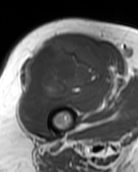
MRI of an extremity soft-tissue mass, one axial slice; position 69 of 99 along the scan axis; MR volume resampled by the dataset authors to the PET/CT grid (not the native acquisition matrix); 3.27 mm slice thickness; 138 × 172 image matrix, field of view 135 × 168 mm. Female patient. From the clinical record (not read from this slice): histological type: pleiomorphic undifferentiated sarcoma; grade: high; site of the primary tumour: right quadricep.
Annotated regions visible in this slice (expert contour drawn on MRI and transferred to this co-registered scan by the dataset authors):
- gross tumour volume including surrounding oedema: bounding box (x1, y1, x2, y2) in pixels: (21, 39, 107, 124)
- gross tumour volume (mass): (21, 39, 107, 124)